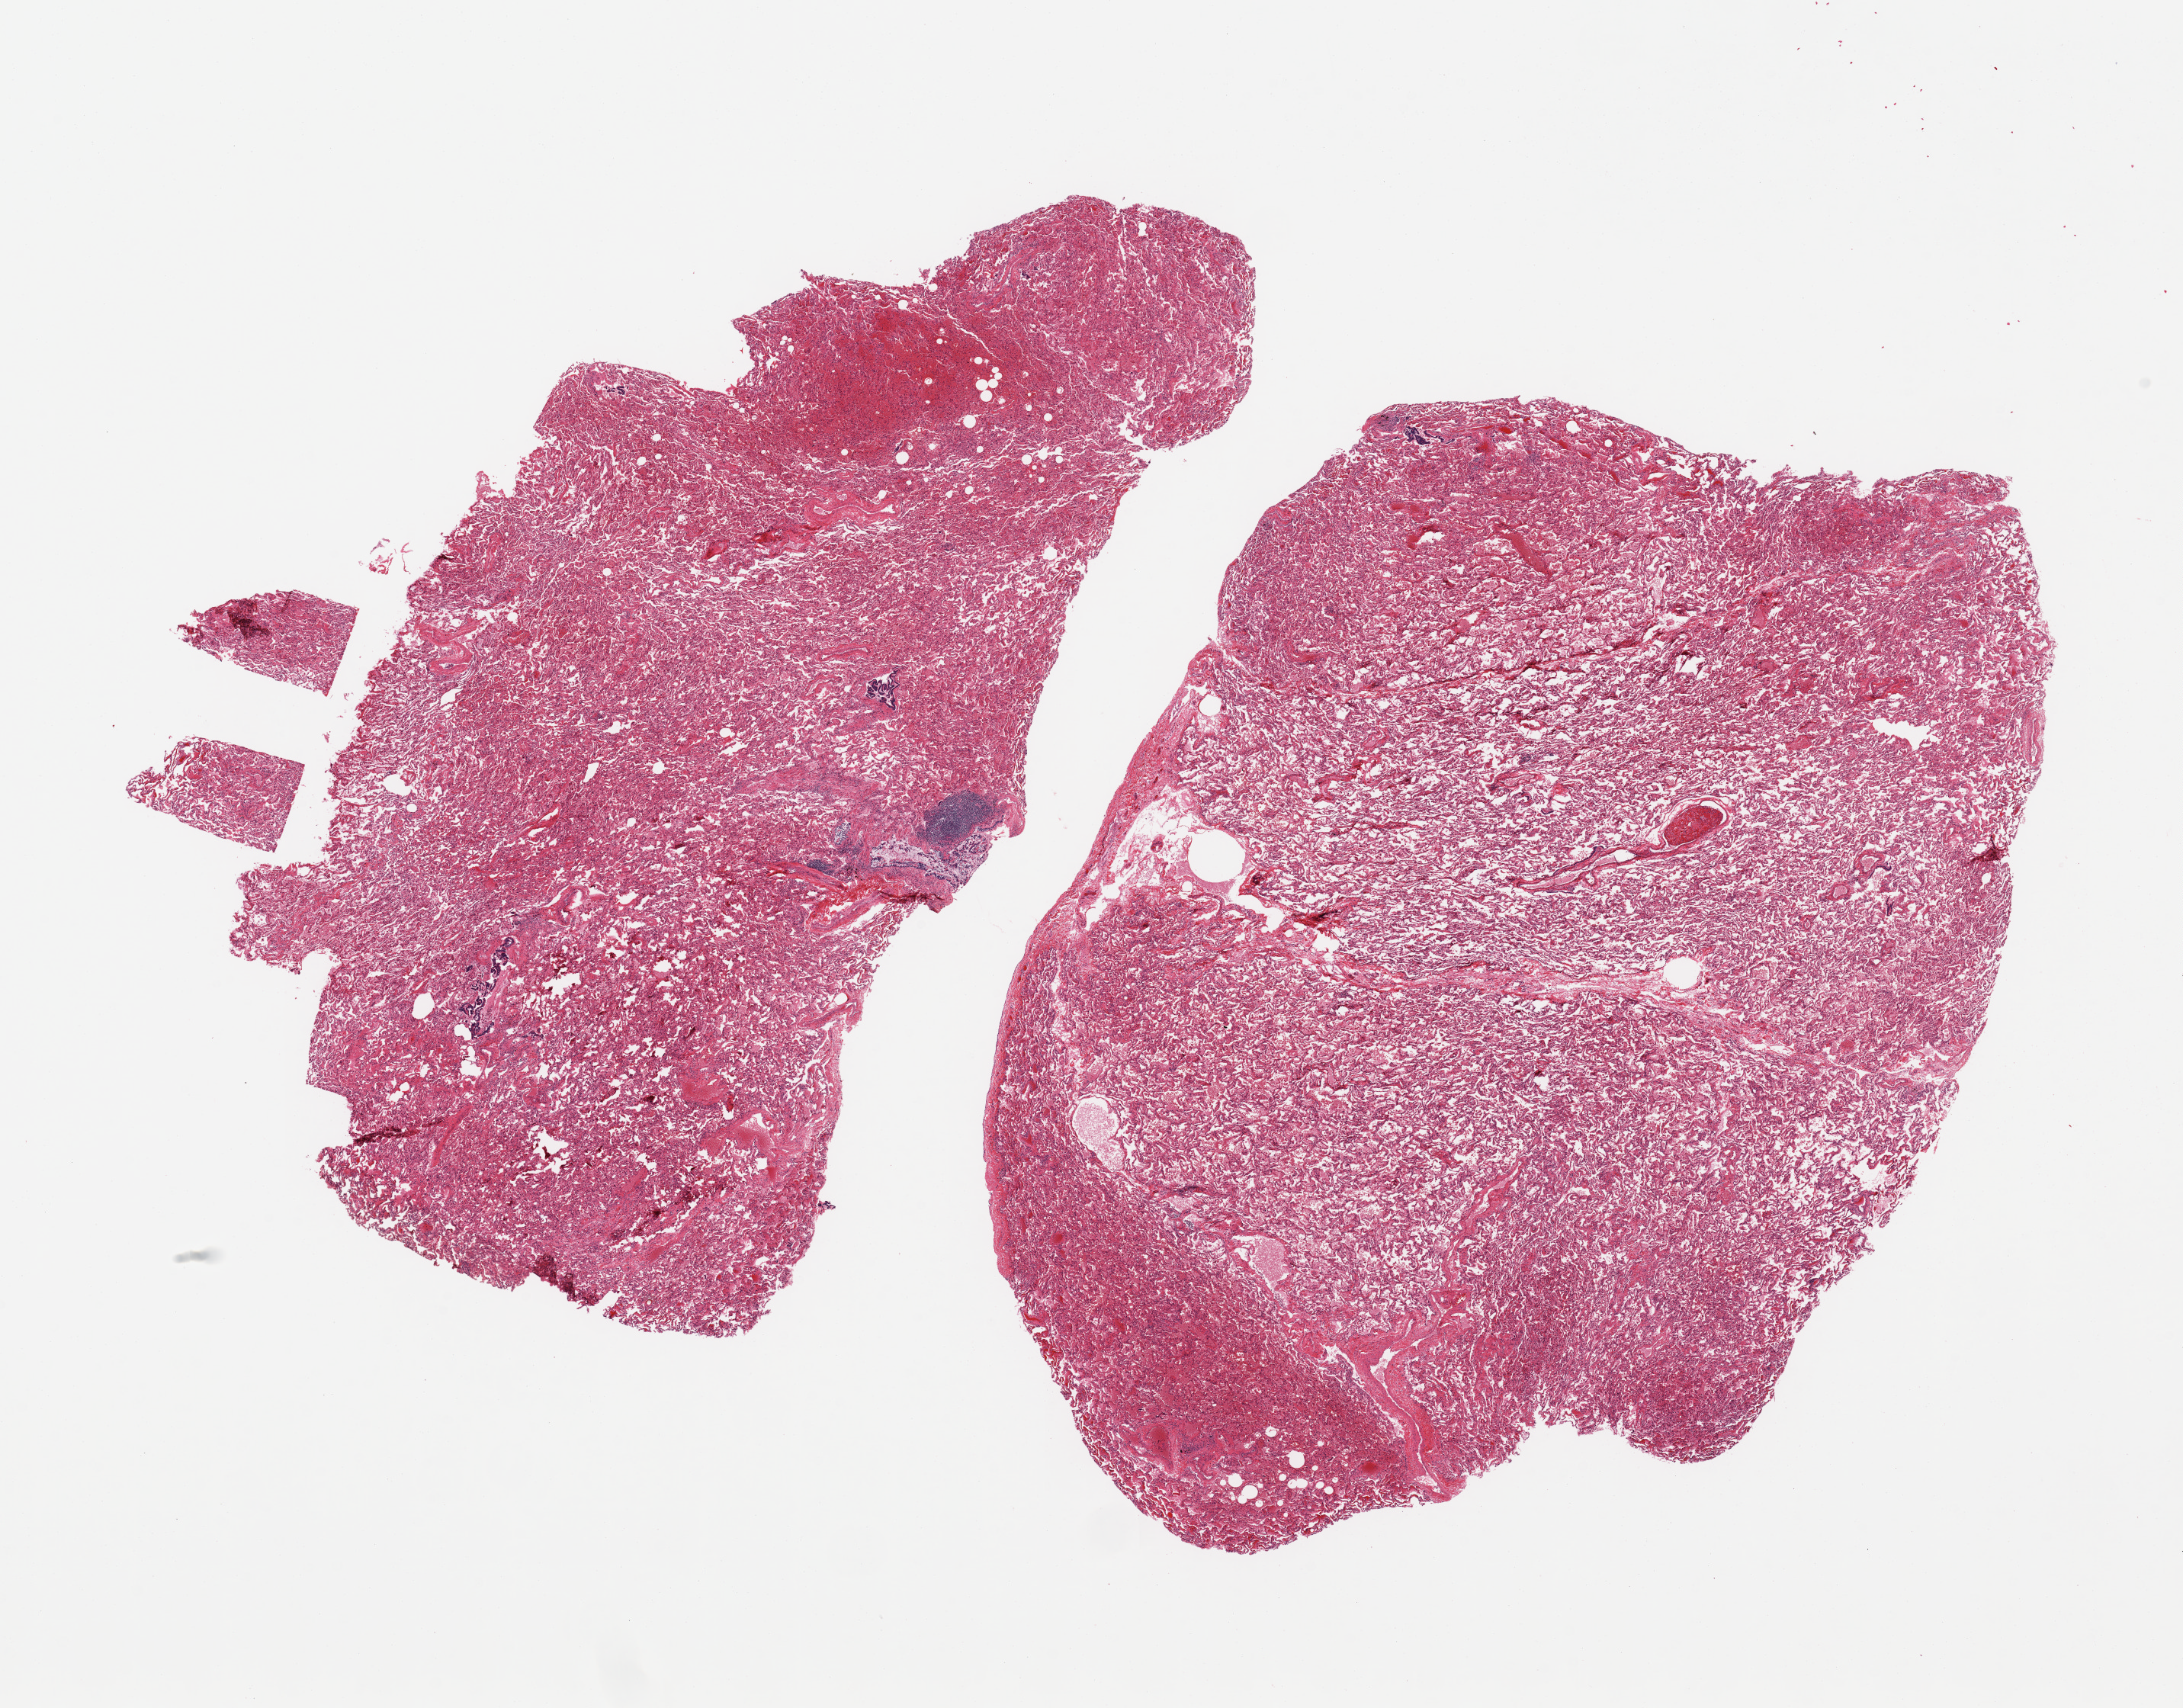
H&E whole-slide image, low-resolution overview of the scanned area, about 22.6 x 17.7 mm. PAXgene-fixed paraffin-embedded (PFPE) section. Section of lung (target tissue). Tissue donor sample.
Pathologist's review note for this sample: 2 pieces, patchy mild edema.